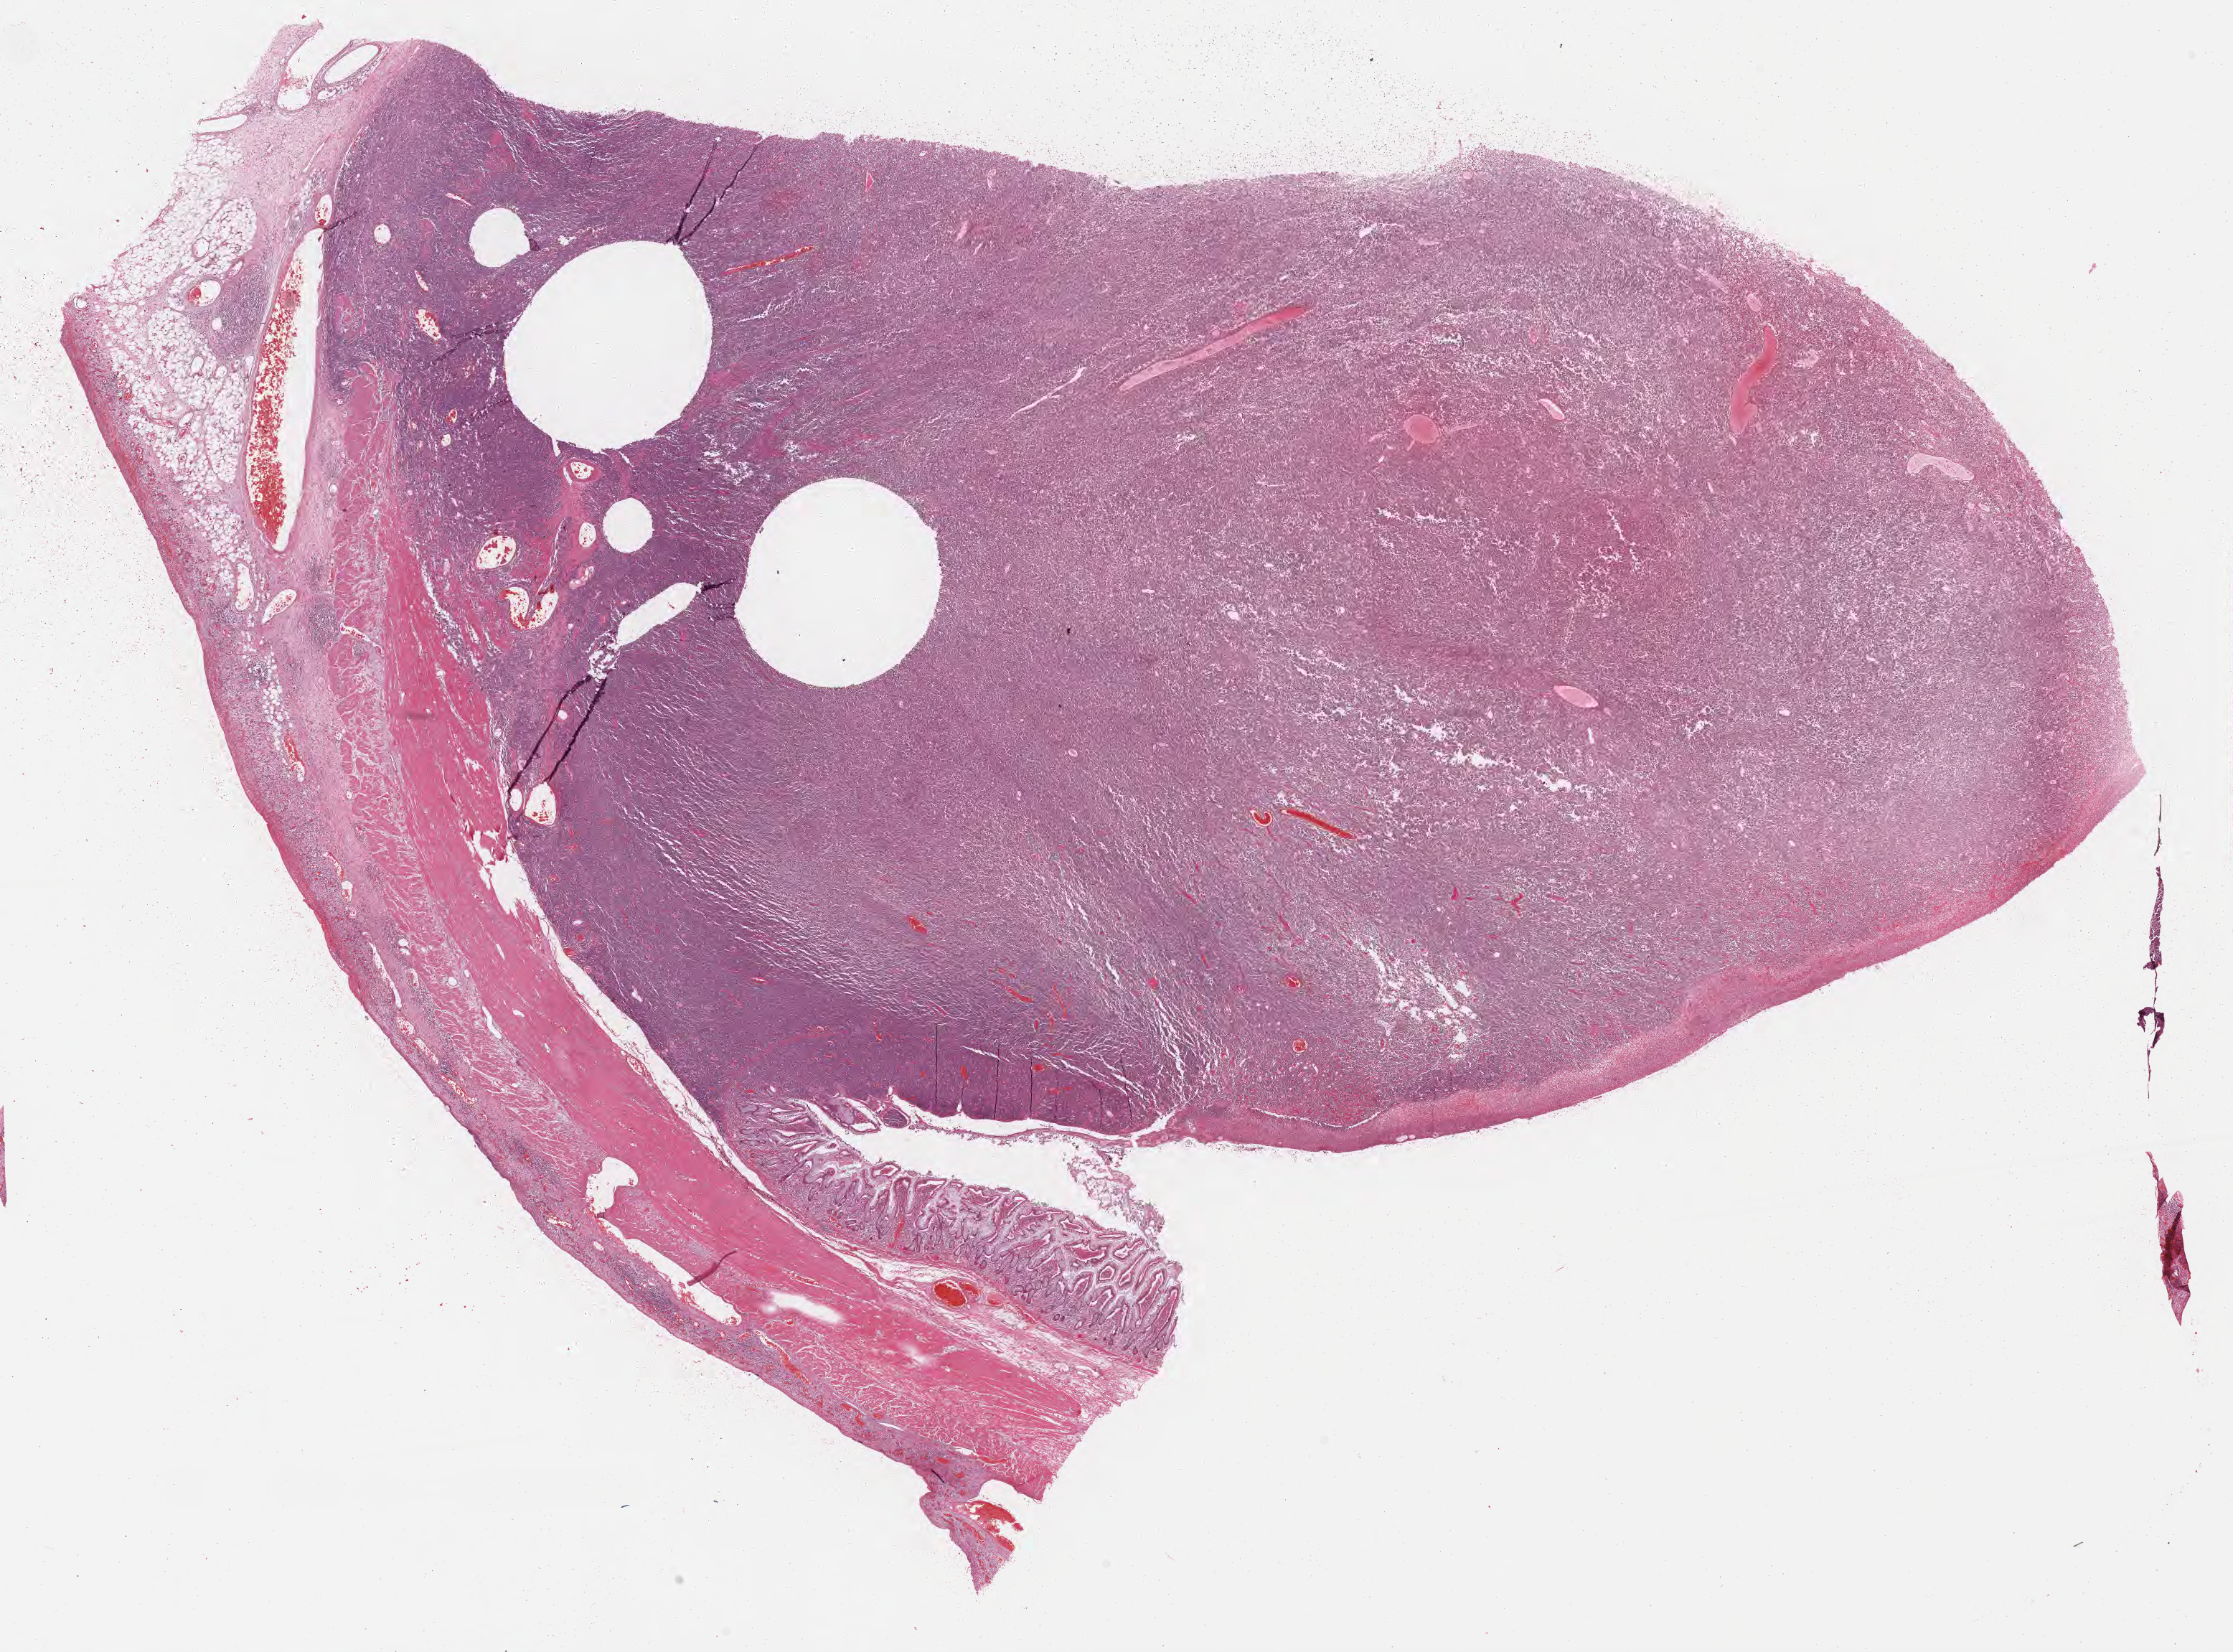
Digitized haematoxylin and eosin-stained section — shown as a low-resolution overview of the whole scanned area (about 25.2 x 18.6 mm); formalin-fixed paraffin-embedded section; primary tumor. Female patient, age 15 years. Composition of this section per pathologist review: tumor cells 75%, tumor nuclei 90%, stromal cells 10%, necrosis 0%, normal cells 15%. Inflammatory infiltration, as recorded: lymphocyte infiltration 70%, monocyte infiltration 15%, neutrophil infiltration 0%.
Section: top of the tissue portion. Ann Arbor stage (patient): Stage IV. Diagnosis: Burkitt lymphoma, NOS.